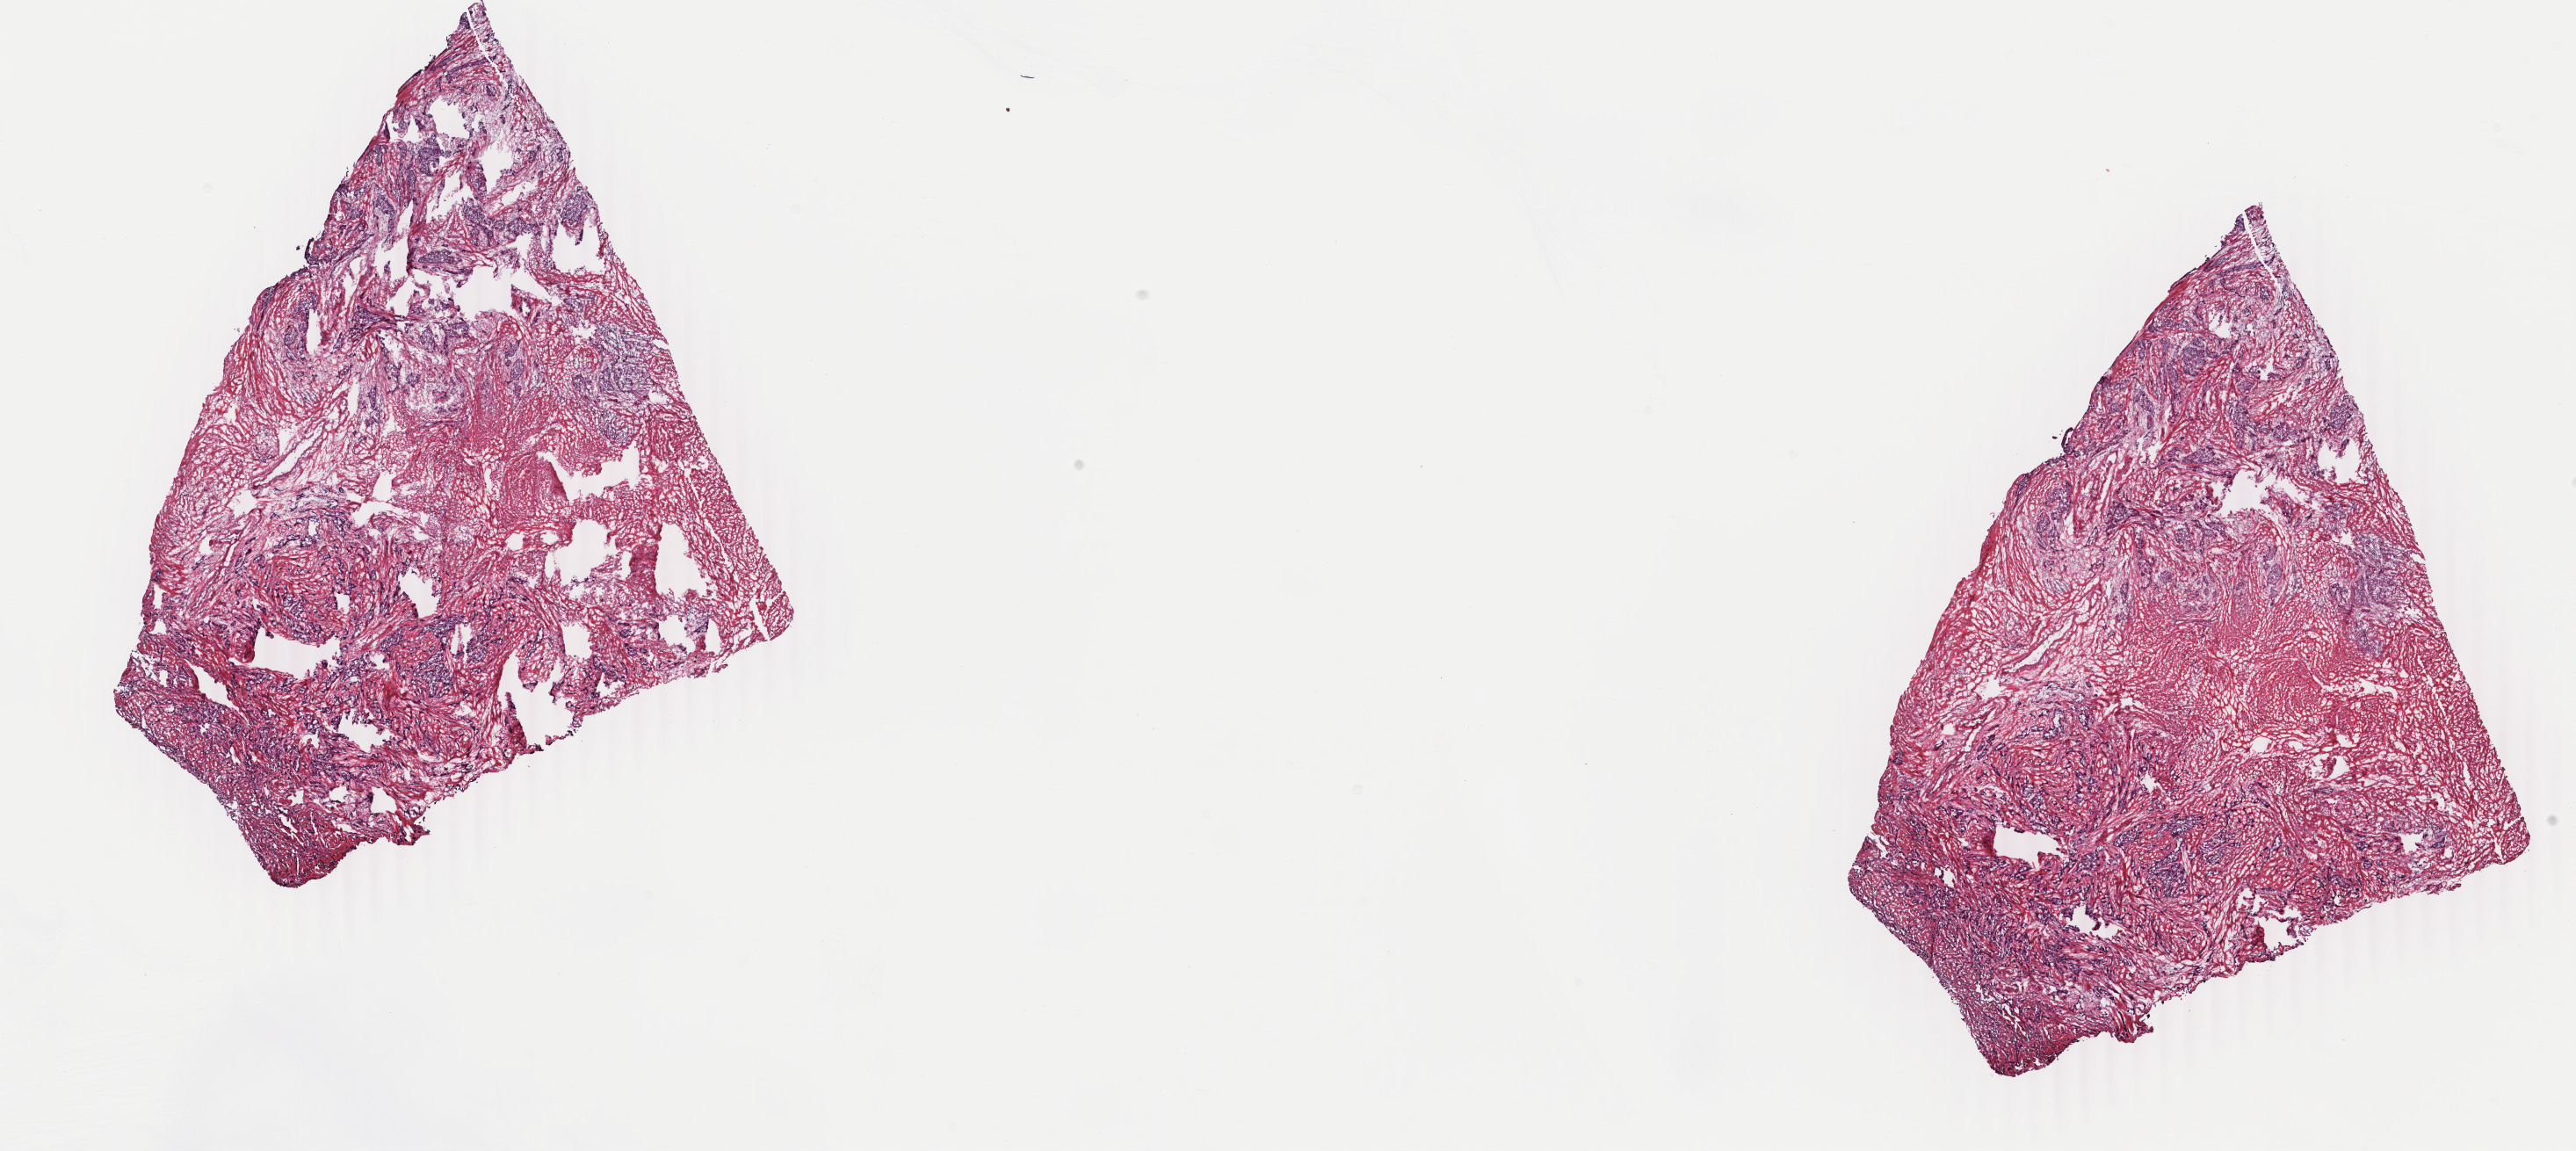
Whole-slide histology image, Hematoxylin and eosin (H&E) stained — low-resolution overview of the scanned area, about 23.3 x 10.4 mm (acquisition: 40x scan). Frozen section from the top of the tissue portion. Sample: primary tumour, cervix. Patient: female, age at initial diagnosis 60 years. Histologic grade: G2 (moderately differentiated). Composition of this section per pathologist review: tumour cells 70%, tumour nuclei 70%, normal cells 0%, stromal cells 30%, necrosis 0%. Infiltration values recorded for this section: lymphocyte infiltration 40%, monocyte infiltration 20%, neutrophil infiltration 20%.
Lymph nodes positive (case pathology): 0 of 18 examined. FIGO stage: IA1. Pathologic diagnosis: Squamous cell carcinoma, NOS (cervix uteri).